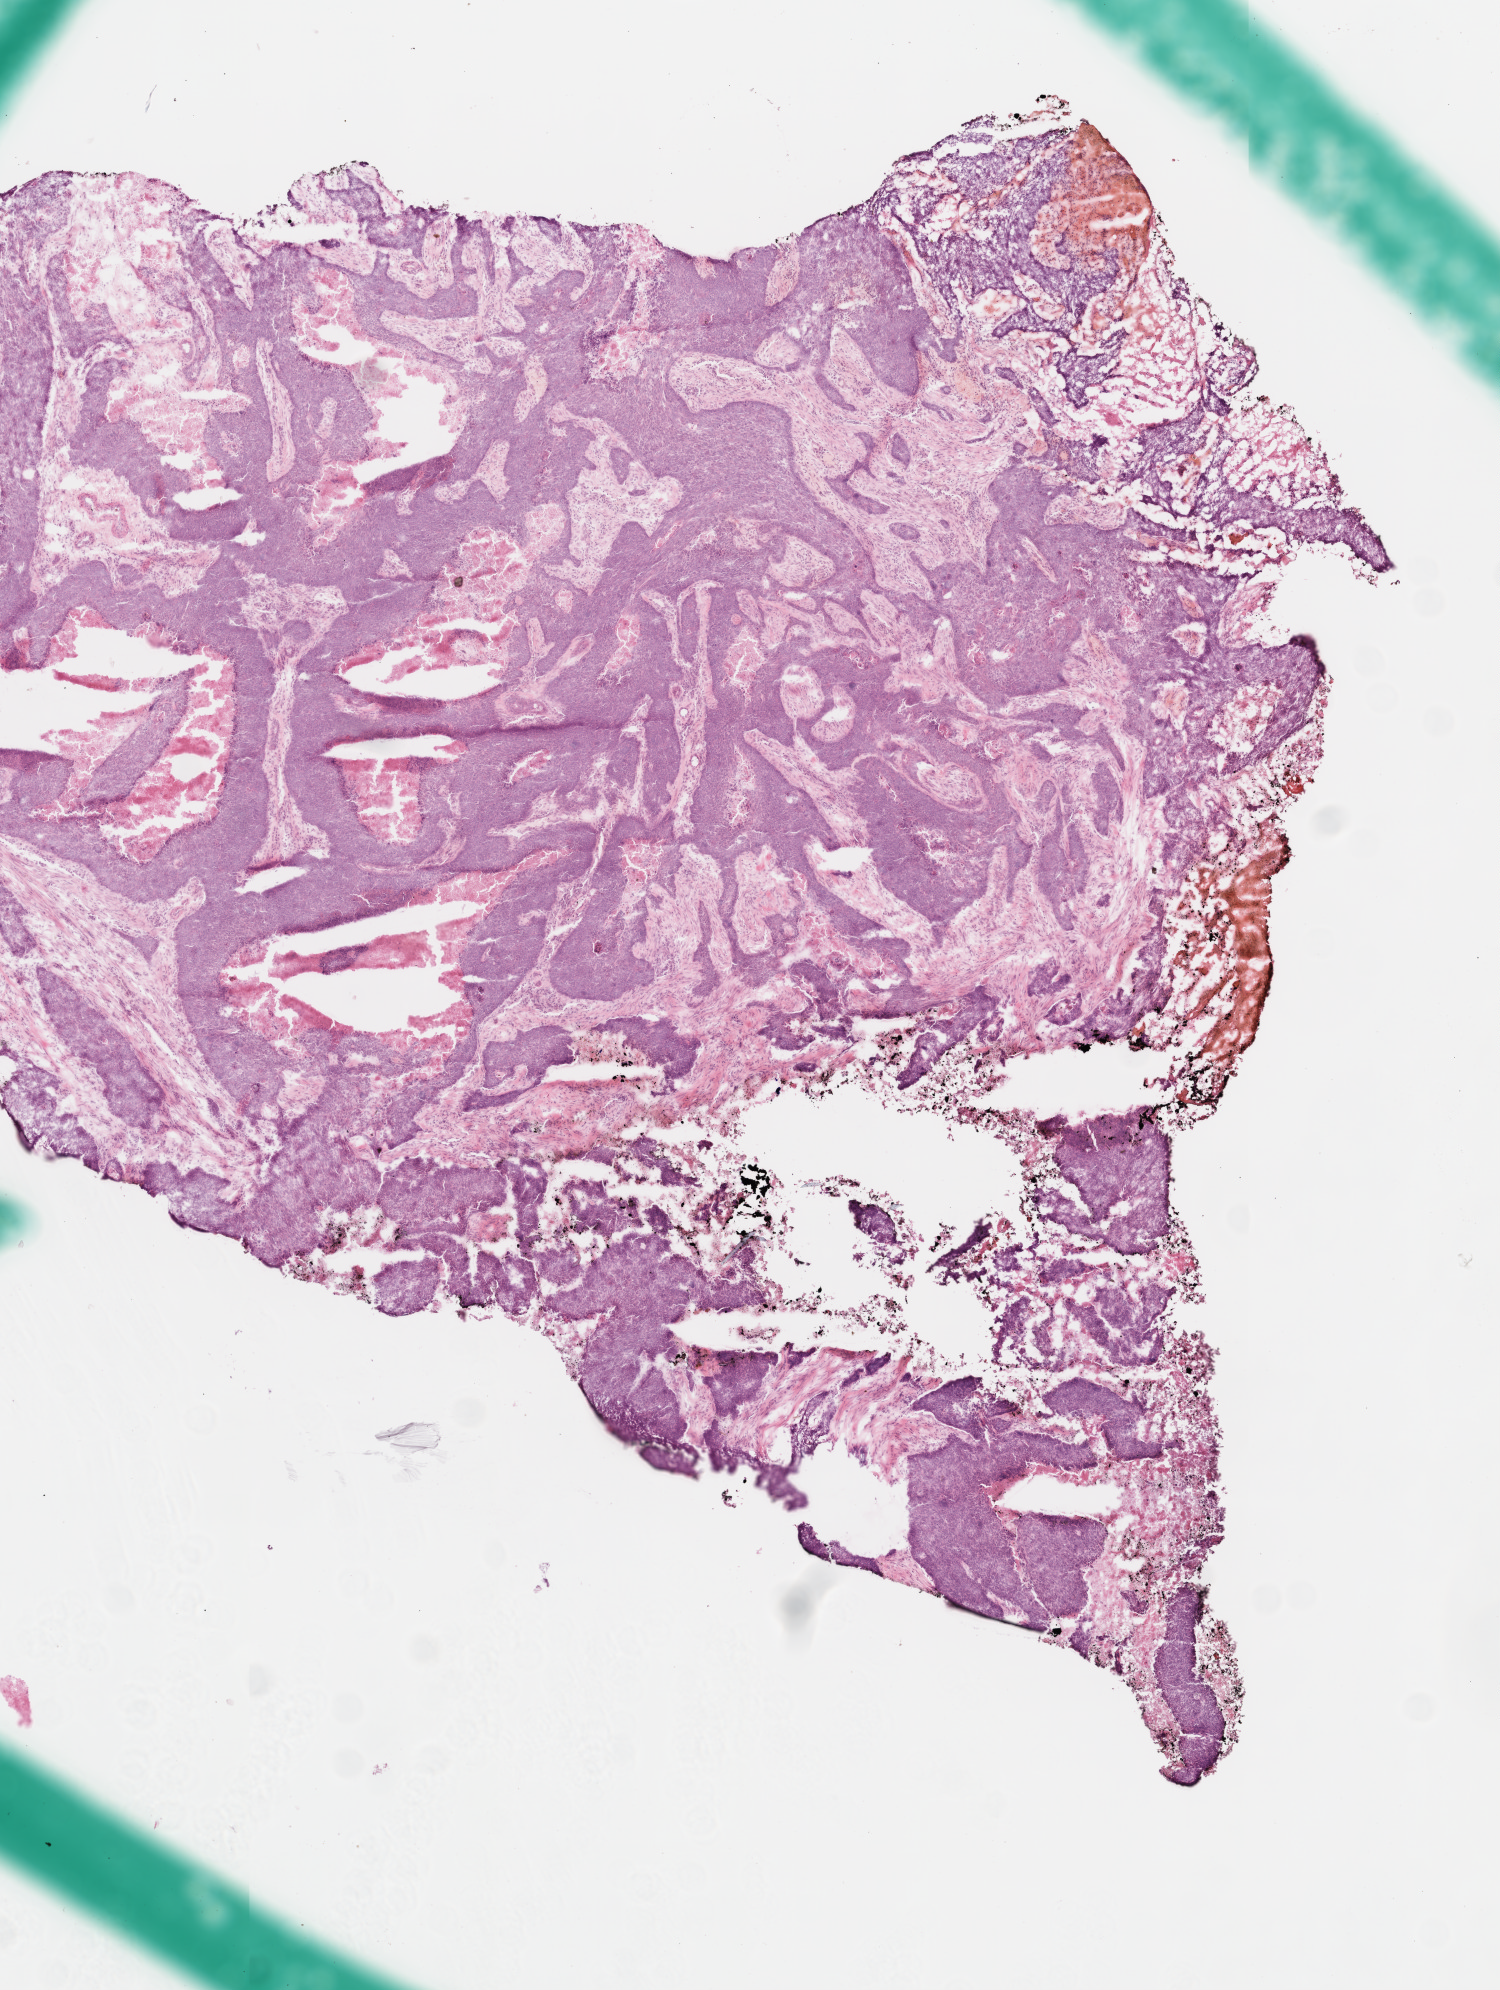
Digitized H&E-stained tissue section (whole slide) — shown as a low-resolution overview of the whole scanned area (about 6.0 x 8.0 mm), frozen section from the top of the tissue portion, head and neck, primary tumour sample. Male patient; age at initial diagnosis 50 years. Histologic grade: GX (grade cannot be assessed). Pathologist review of this section (percent, as recorded): tumour cells 80%, tumour nuclei 90%, normal cells 0%, stromal cells 13%, necrosis 7%. Inflammatory infiltration, as recorded: lymphocyte infiltration 2%, neutrophil infiltration 1%.
- histologic diagnosis: Squamous cell carcinoma, NOS
- laterality: right
- AJCC pathologic stage: III